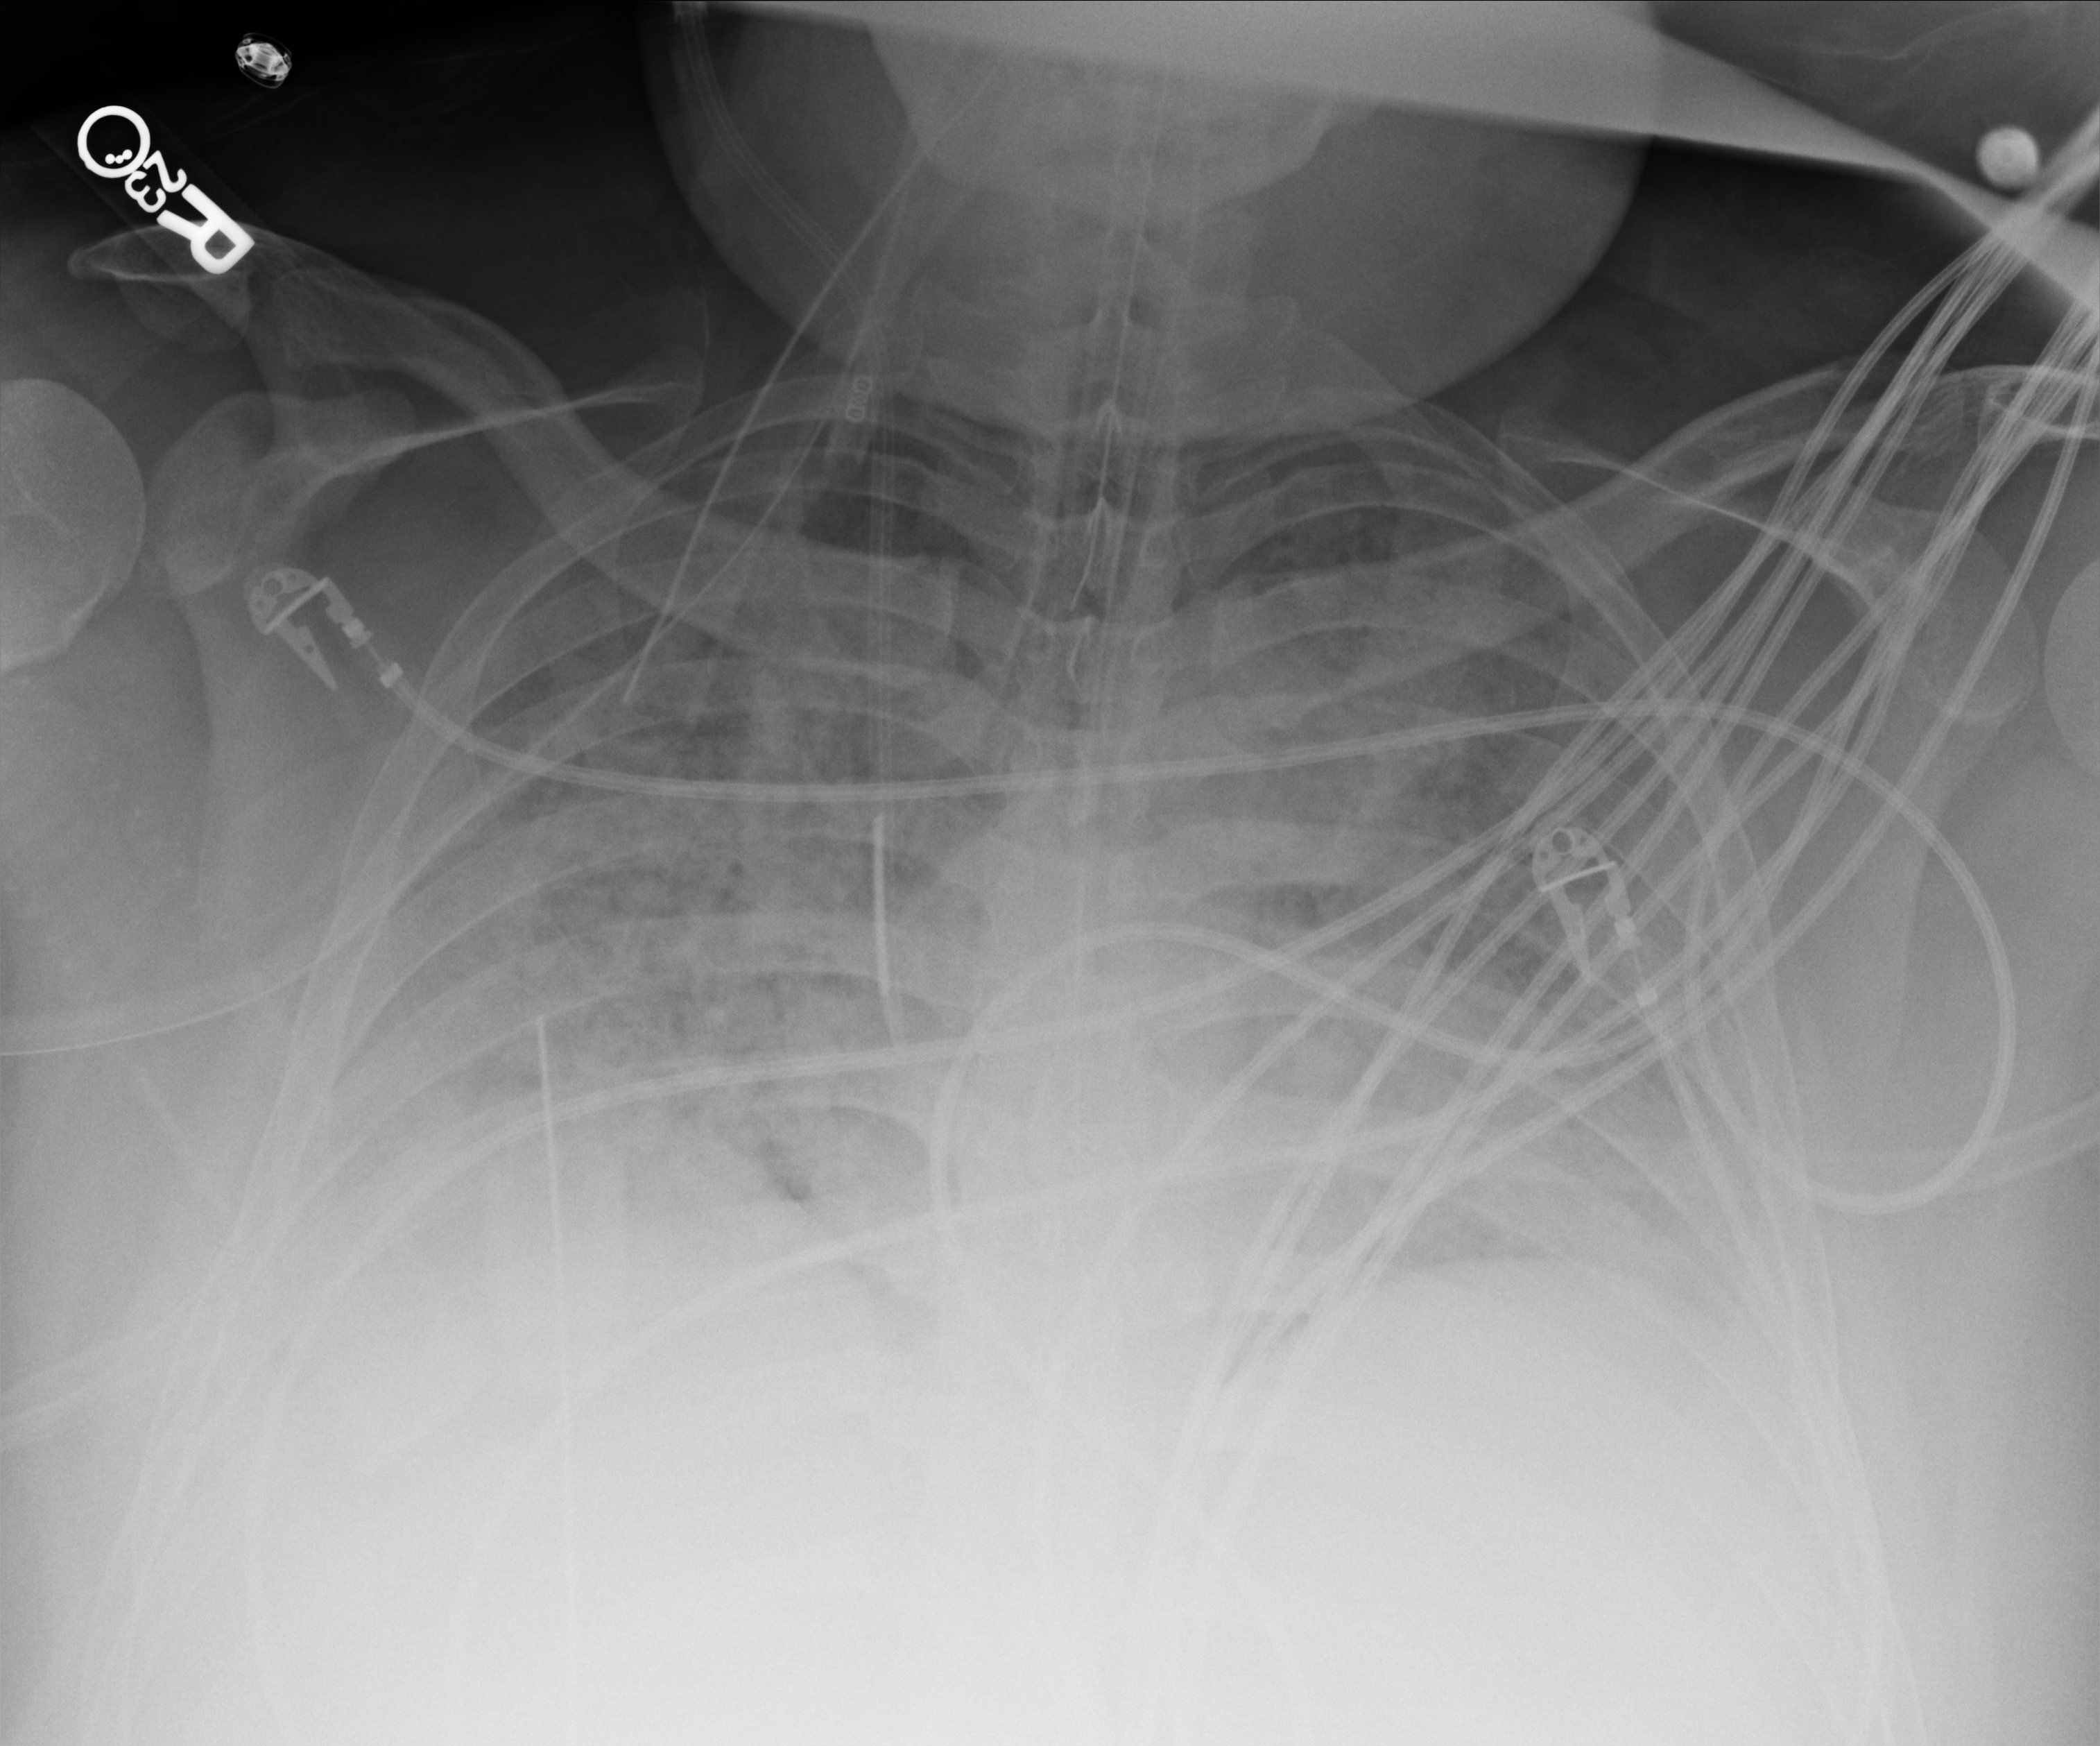
Portable chest radiograph, anteroposterior (AP) projection. Patient hospitalised with COVID-19, aged 18–59 years.
Admission-level facts for this patient (not findings on this image; timing relative to this image not recorded): mechanically ventilated during this hospital stay: yes; admitted to intensive care during this hospital stay: yes; hypertension (admission record): no.